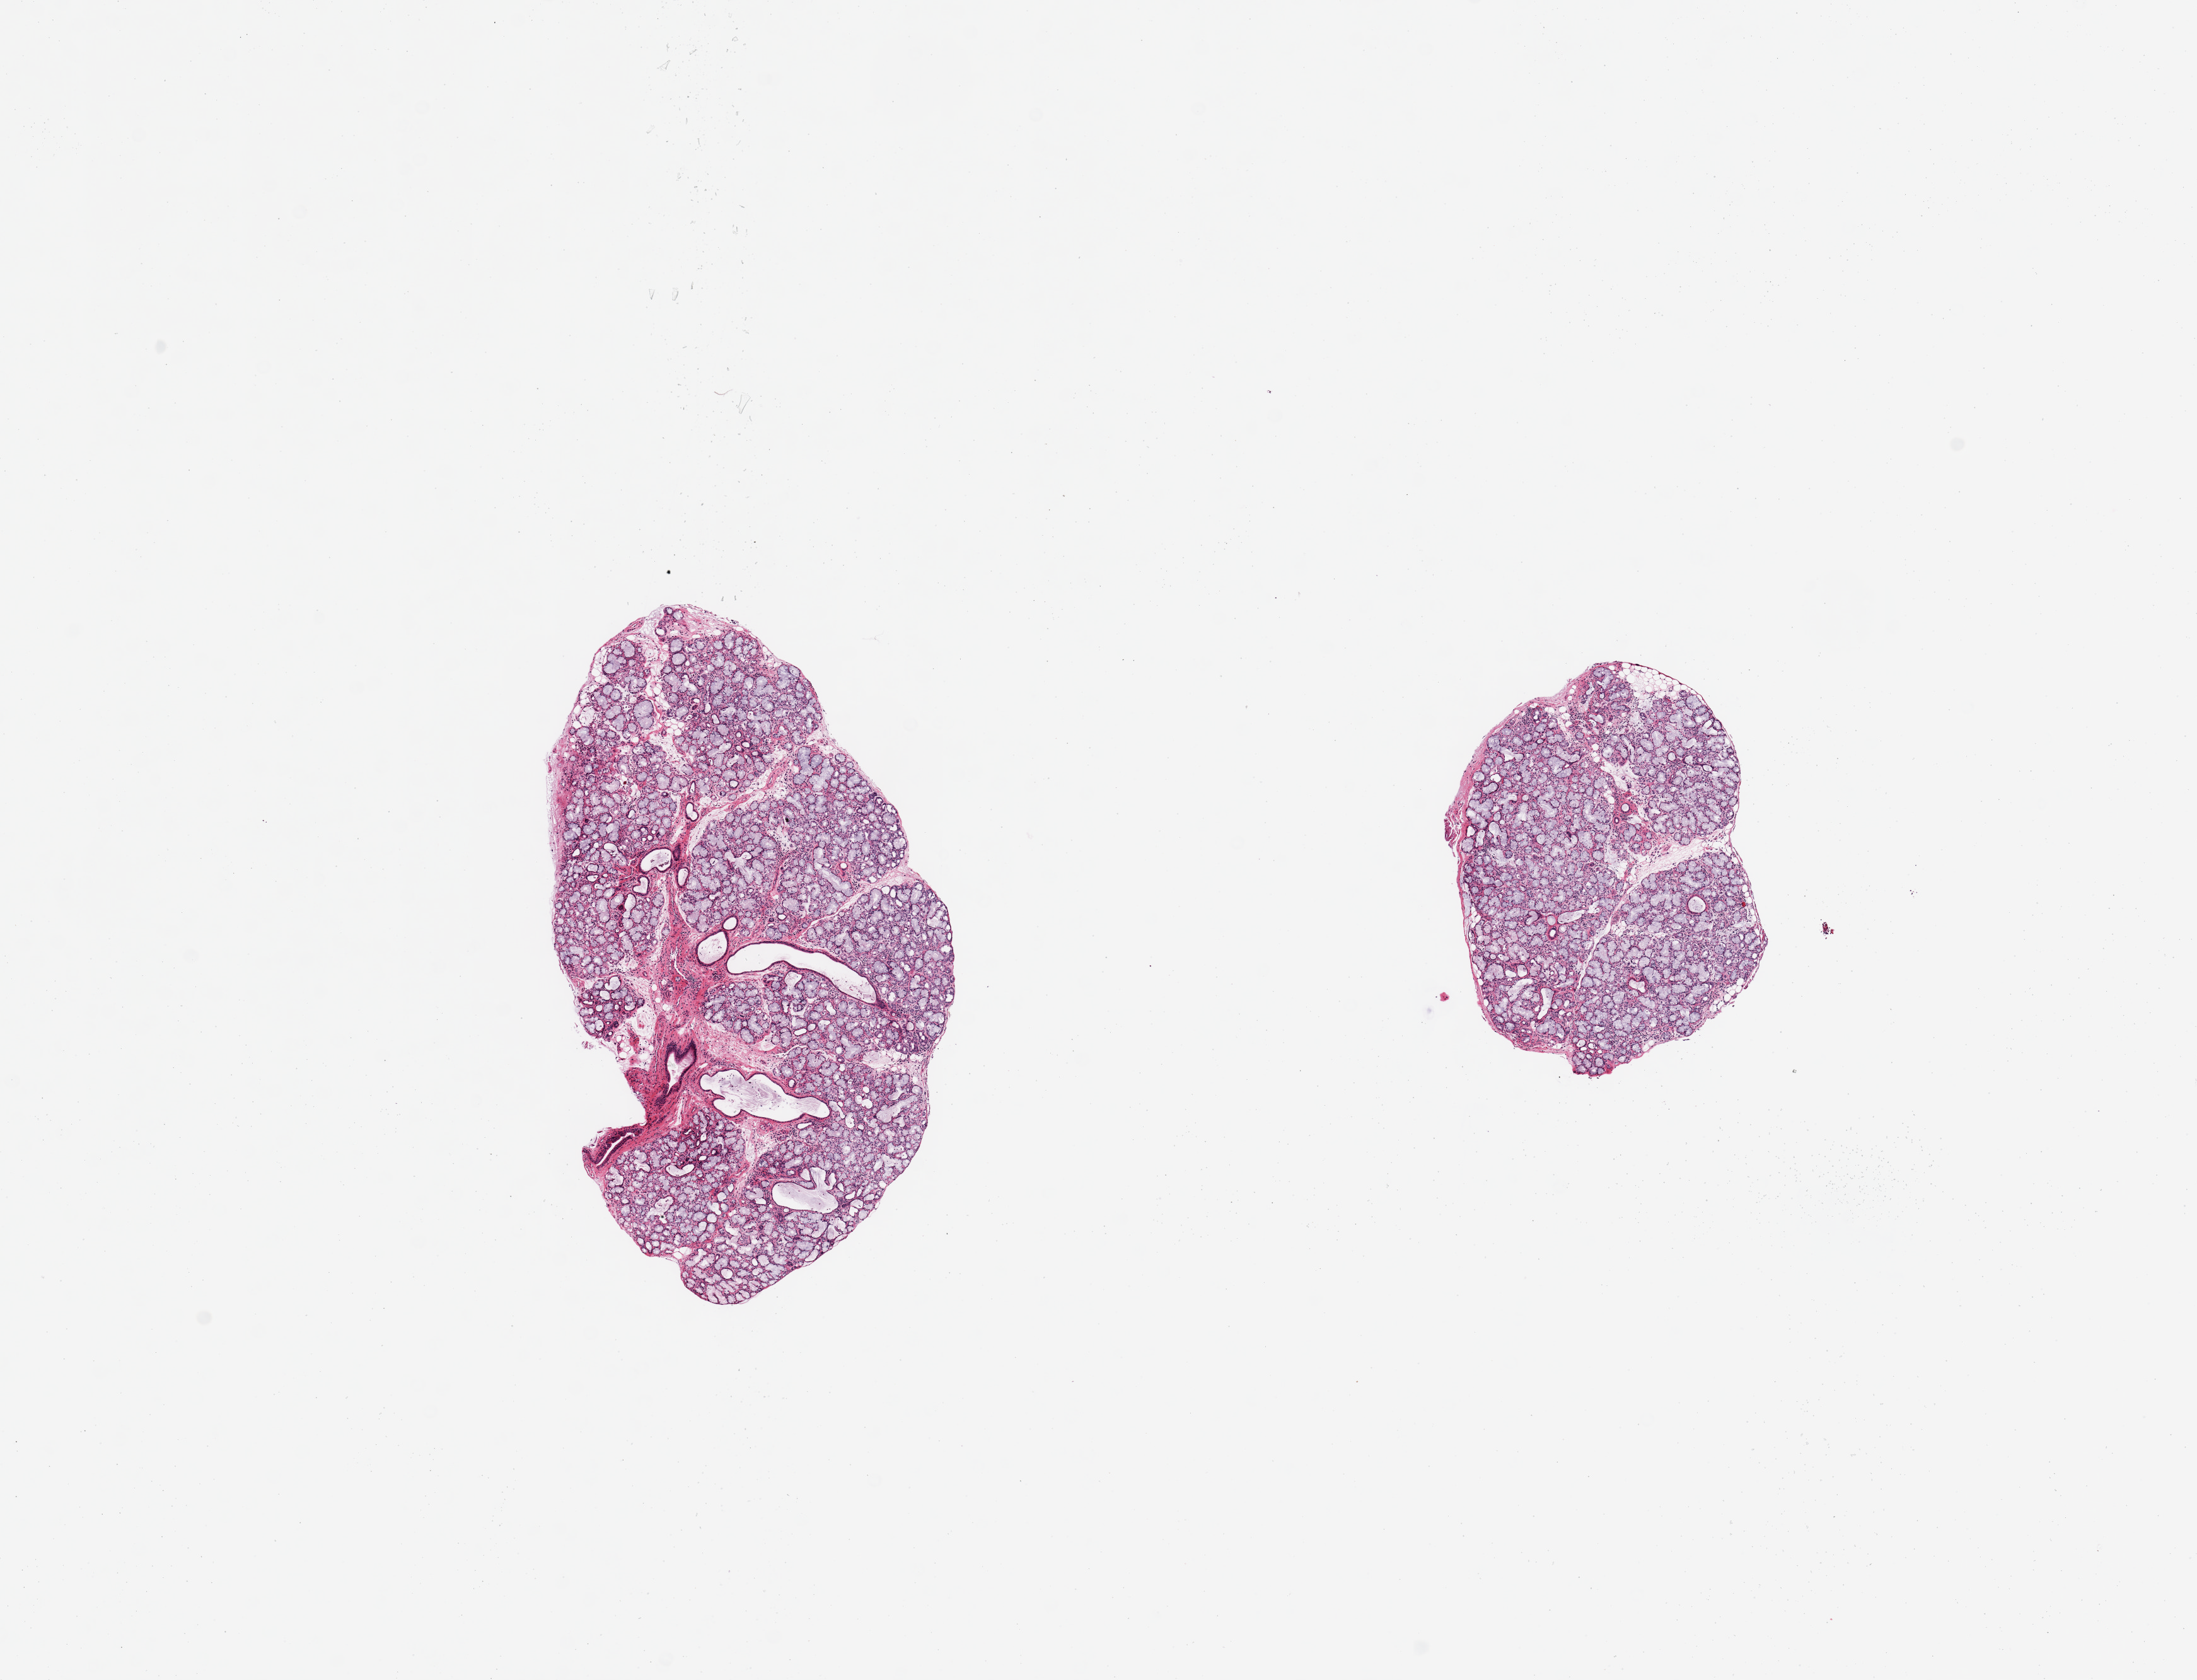
Whole-slide image, haematoxylin and eosin stain, brightfield — a low-resolution overview of the entire scanned area, about 13.8 x 10.5 mm, PAXgene-fixed paraffin-embedded (PFPE) section, sampled site (target tissue): minor salivary gland, donor tissue sample. Donor sex: female.
Review note (as recorded): 2 pieces, glandular elements essentially 100% of specimen.